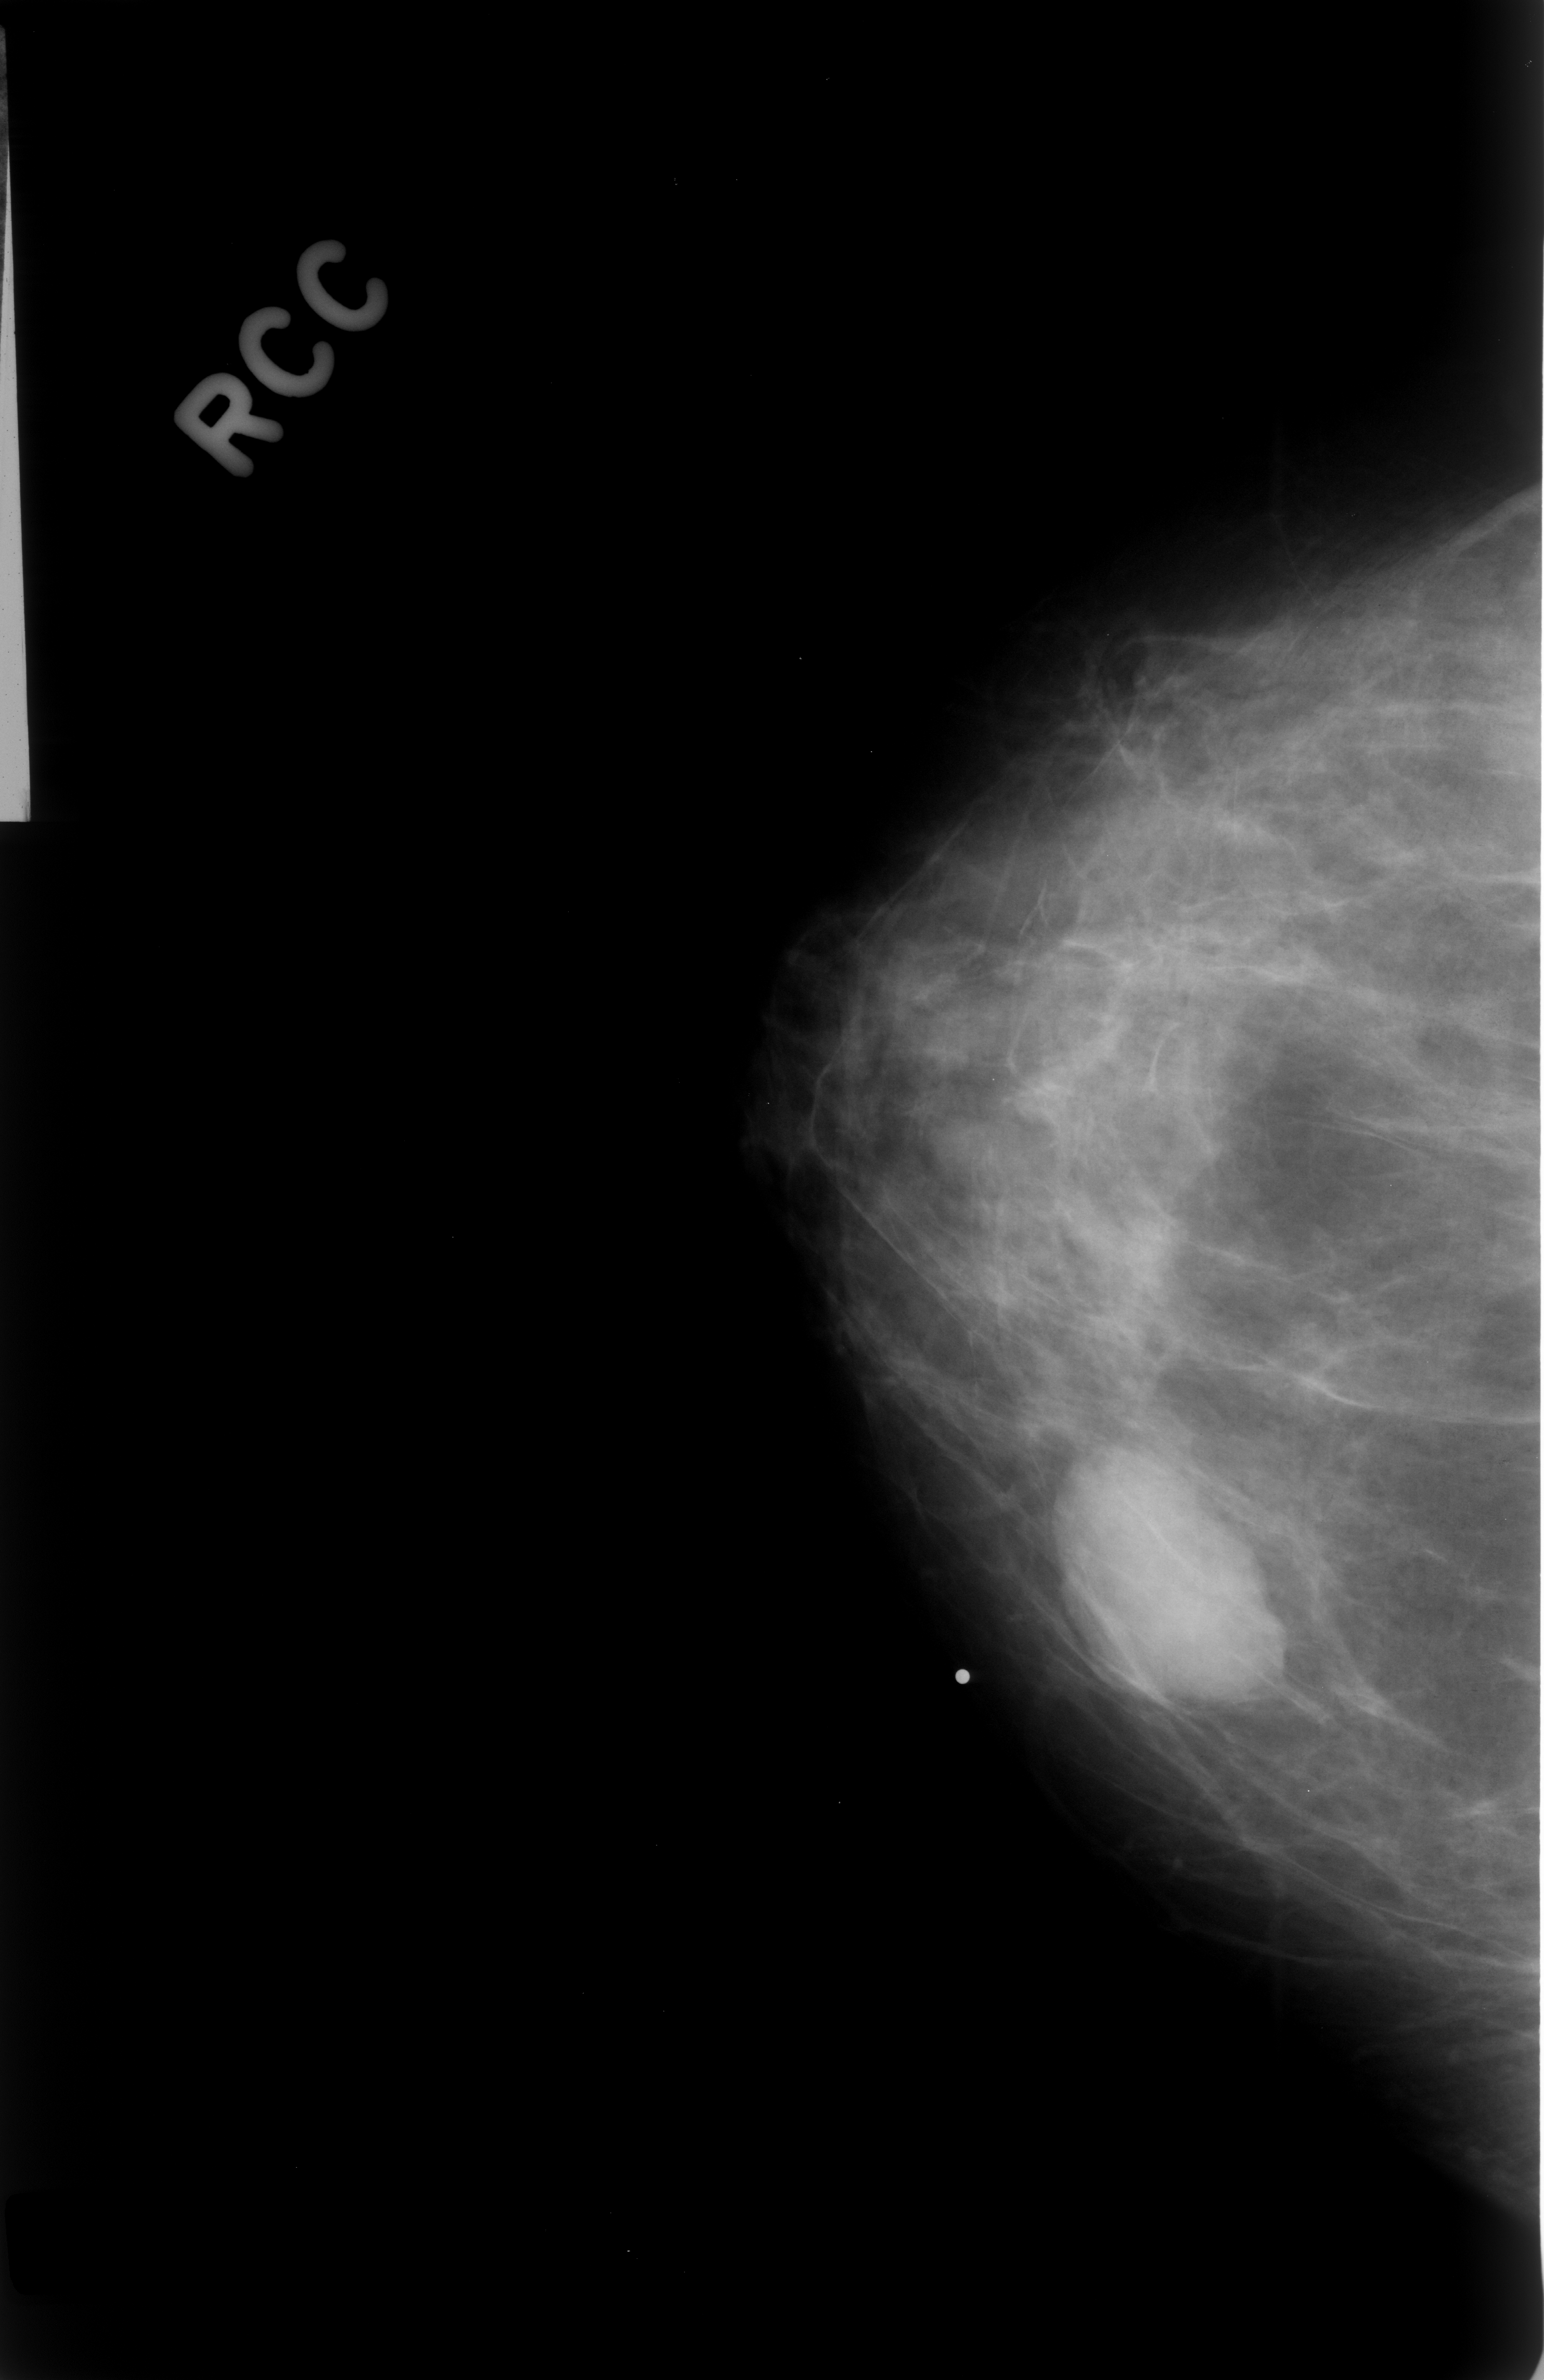
Scanned film-screen mammogram; right breast; craniocaudal (CC) view; breast composition: scattered fibroglandular densities (BI-RADS density category 2 of 4); 1544 × 2380 image matrix.
Expert-marked regions of interest on this film, with their recorded descriptors:
- mass, shape oval, margins circumscribed; BI-RADS assessment category 3; pathology result (as recorded, not read from the image): benign: bounding box (x1, y1, x2, y2) in pixels: (1035, 1447, 1288, 1727)